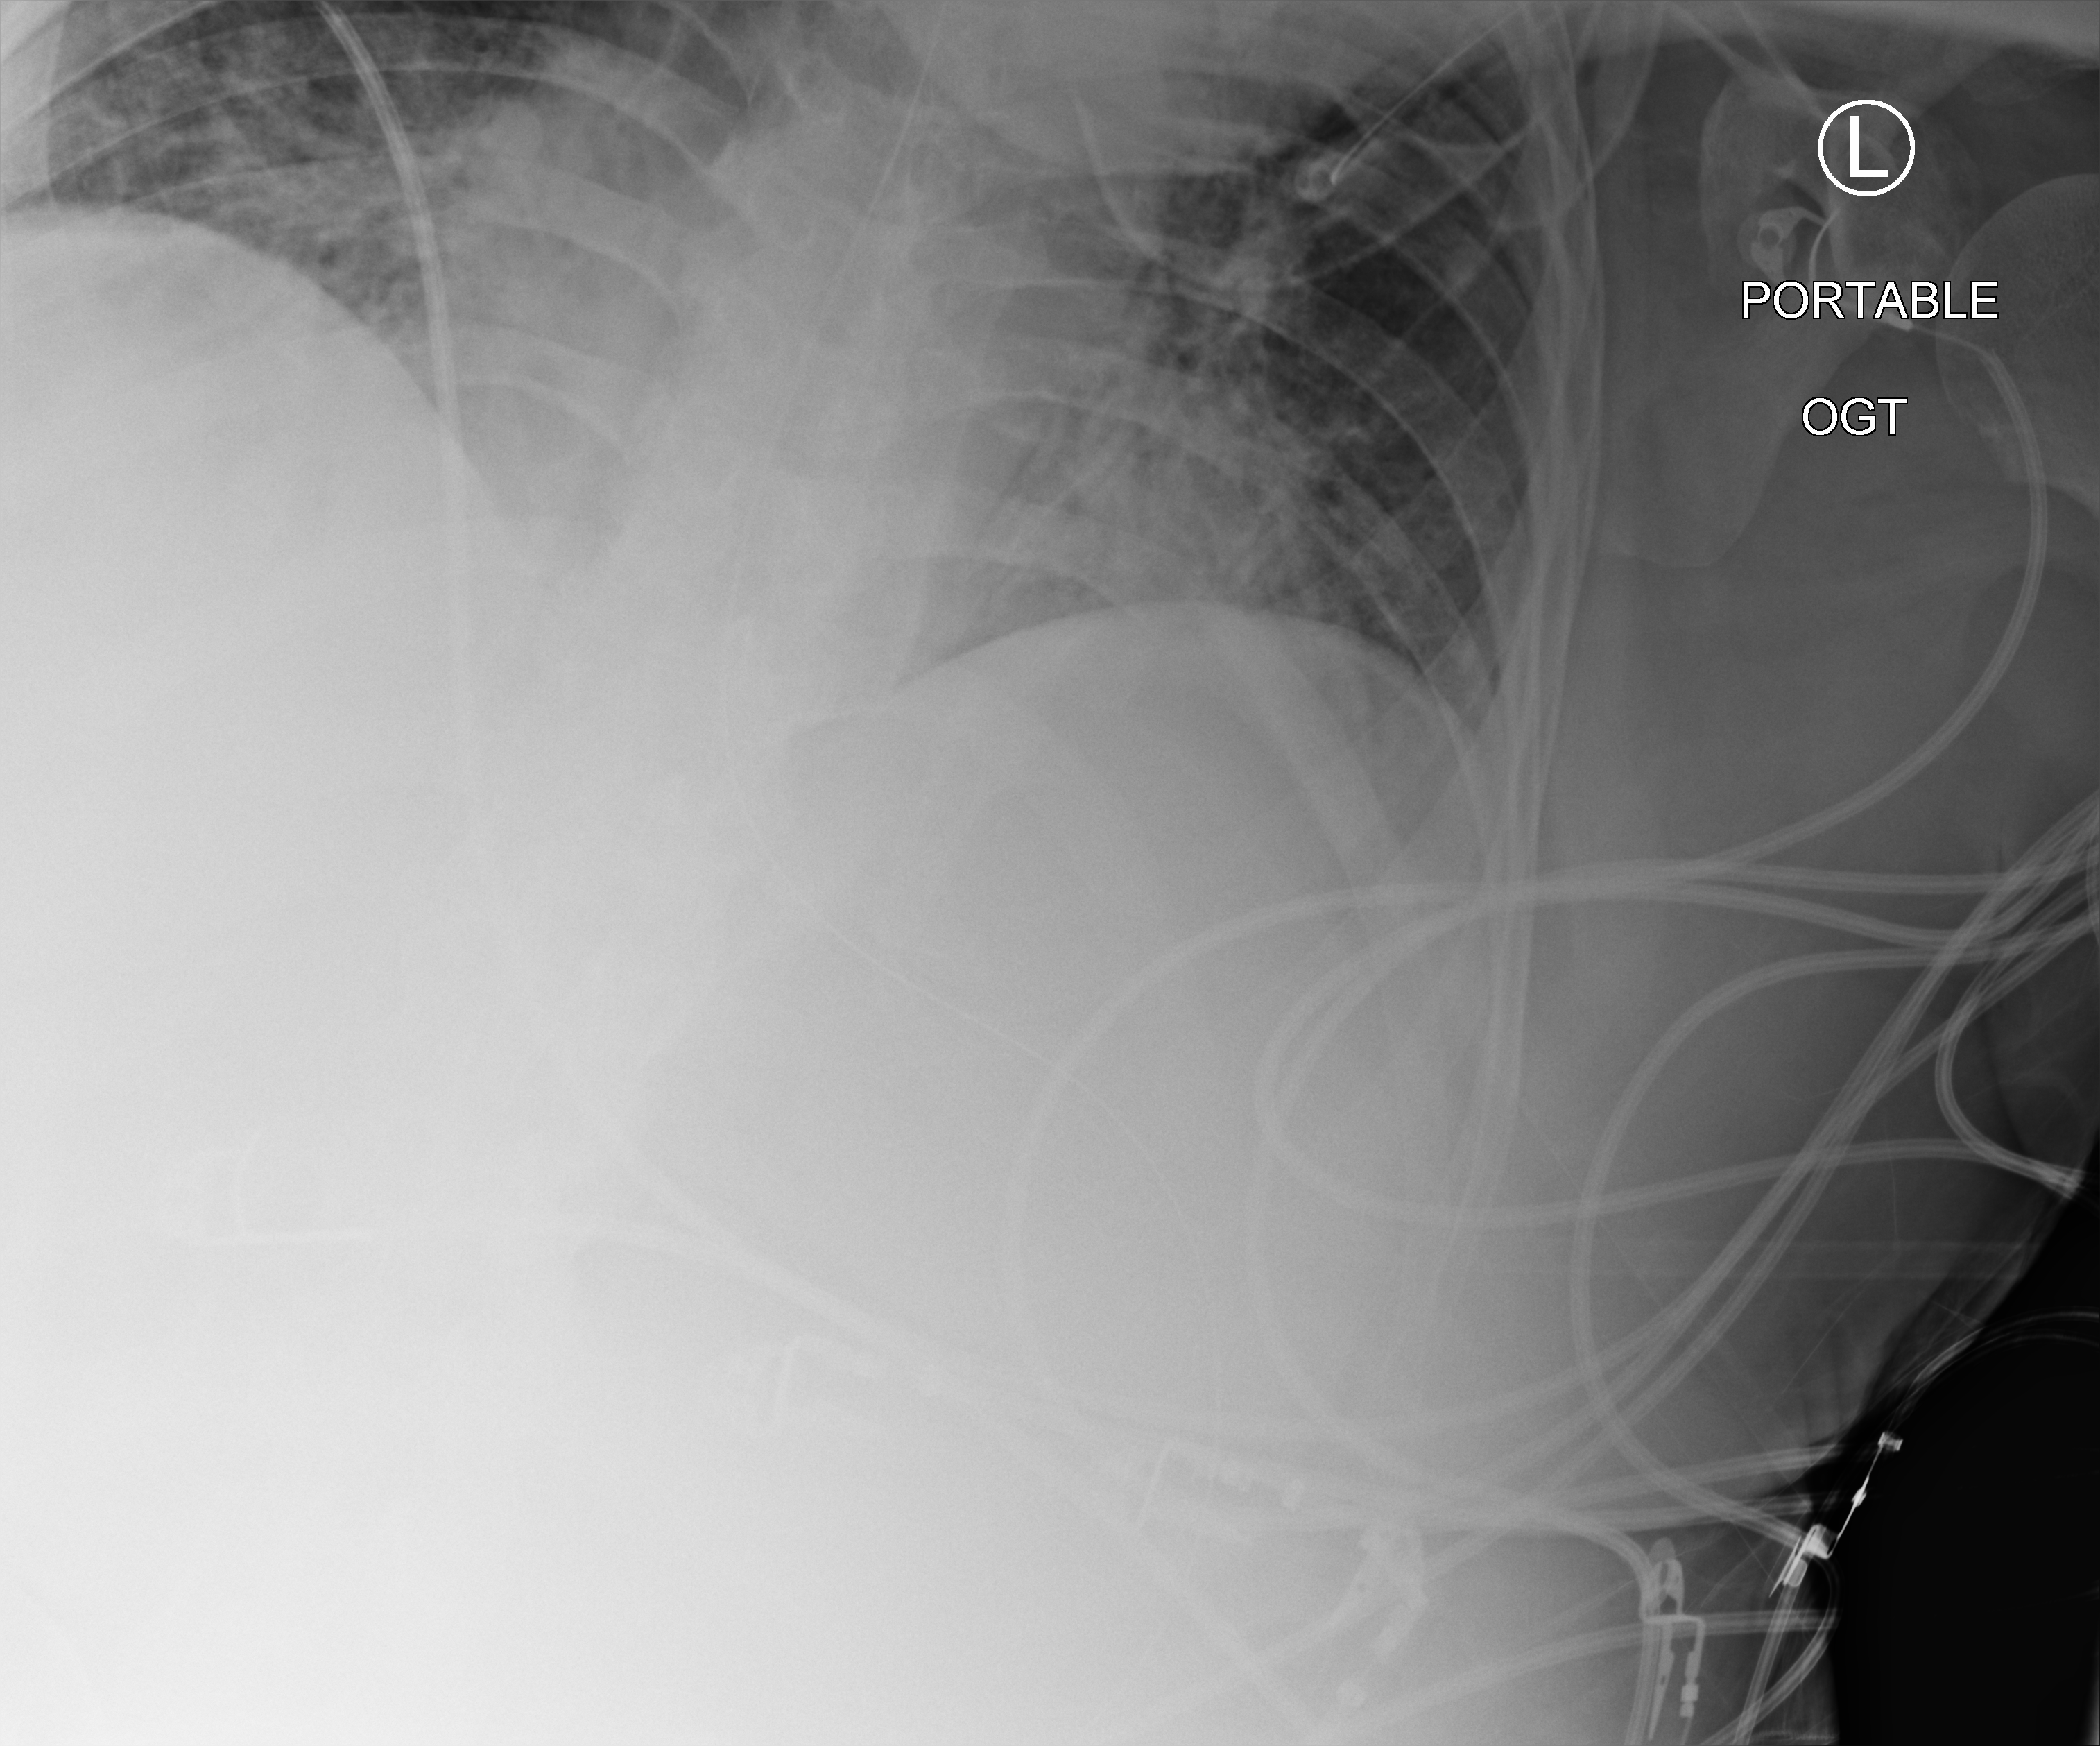
Chest X-ray (portable), anteroposterior (AP) projection. Male patient hospitalised with COVID-19, age 18–59 years.
From the hospital-stay record, not from the radiograph (when in the stay this image was taken is not recorded): other chronic lung disease (admission record): no; admitted to intensive care during this hospital stay: yes.